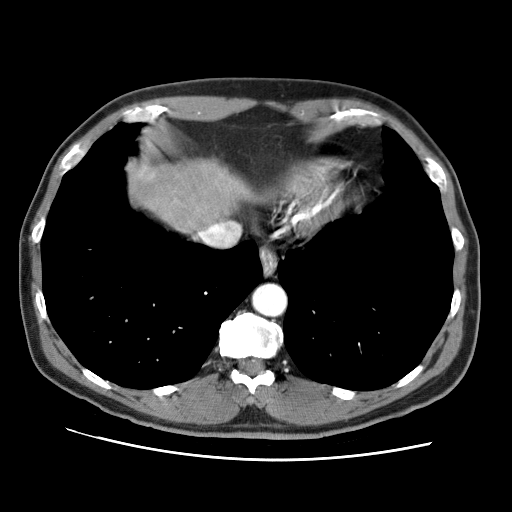
Contrast-enhanced abdominal CT (liver protocol), one axial slice; position 65 of 71 along the scan axis; 120 kVp; soft-tissue window (W 400 / L 40 HU); 512 × 512 image matrix, field of view 360 × 360 mm. Case-level facts recorded for this patient, not image findings: diagnosis: hepatocellular carcinoma (patient treated with transarterial chemoembolisation; whether this scan precedes or follows treatment is not stated here); TNM stage (as recorded): Stage-II; Child-Pugh class: A; tumour differentiation: well differentiated; tumour size: 4.6 cm.
Annotated regions visible in this slice (semi-automatic segmentation, software-assisted and operator-edited):
- liver parenchyma outside the tumour (the mass and vessels are separate outlines, so this box may not span the whole liver): bounding box [x1, y1, x2, y2] px = [128, 161, 248, 228]